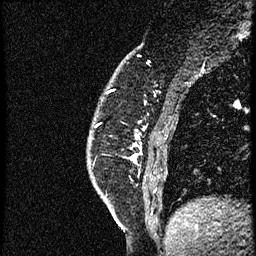
Breast MRI (dynamic contrast-enhanced), one sagittal slice. Slice 14 of 56 in the series (ordered by position). Dynamic contrast-enhanced study with each time point stored as its own series, time point 2 of 4 at this slice position (early post-contrast, ordered by acquisition time). 1.5 T. TE 4.2 ms, TR 18.9 ms. 2 mm slice thickness. 256 × 256 image matrix, field of view 200 × 200 mm. Female patient. From the clinical record (not read from this slice): setting: breast cancer imaged before/during neoadjuvant chemotherapy; receptor status: HER2-positive.
Structures marked on this image (semi-automatic segmentation, software-assisted and operator-edited):
- analysis volume of interest (the breast-tissue region the enhancement analysis was run in; not a lesion): box from (x=134, y=86) to (x=174, y=189) px
- tumour enhancement mask (voxels above the 100 % enhancement threshold inside the analysis volume of interest): (x=135, y=155)–(x=138, y=158)